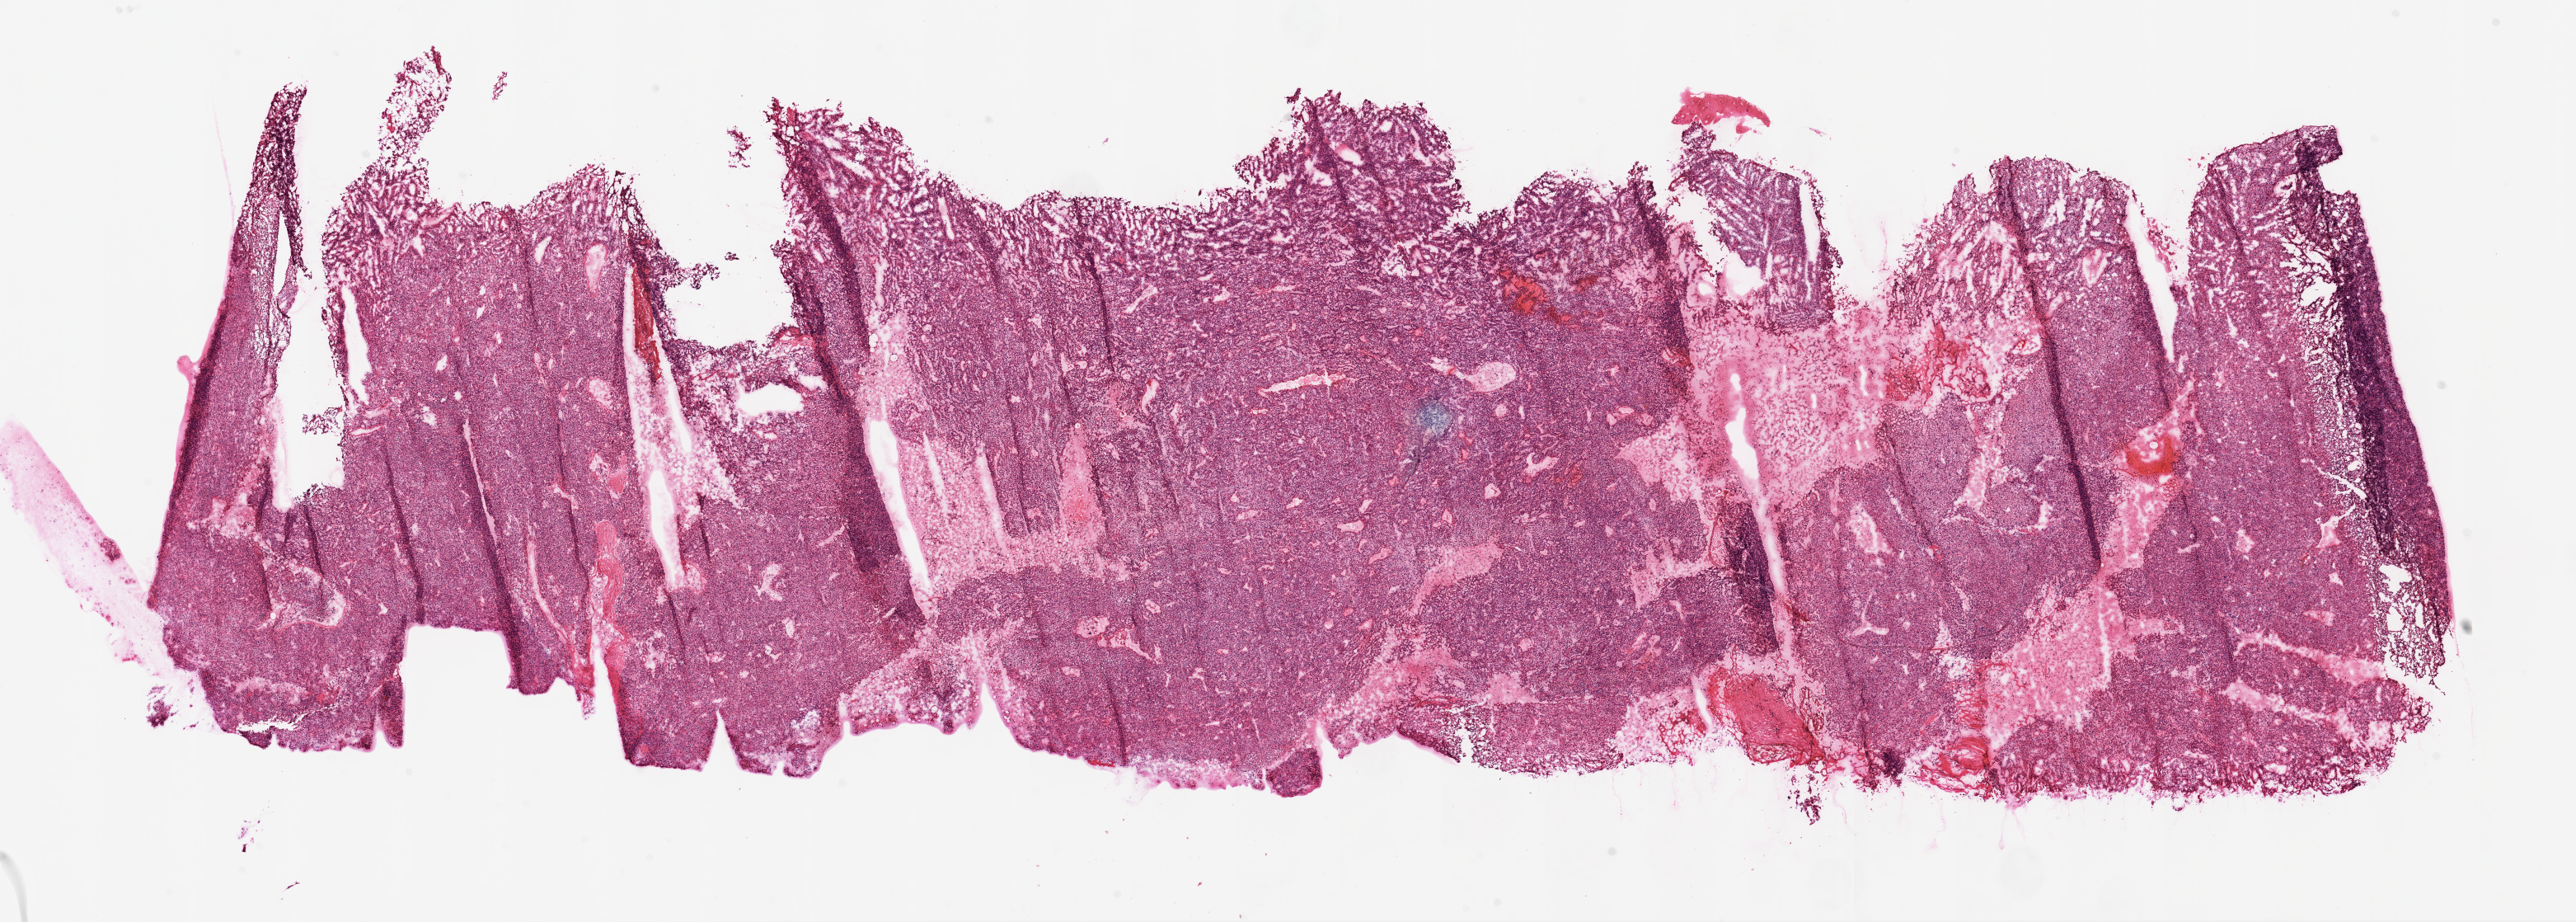
H&E-stained whole-slide image — whole scanned area (about 25.1 x 9.0 mm, from a 20x scan) shown as a low-resolution overview; frozen section from the top of the tissue portion; primary tumour sample from the kidney. Male patient; age at initial diagnosis 67 years.
Diagnosis: Clear cell adenocarcinoma, NOS.